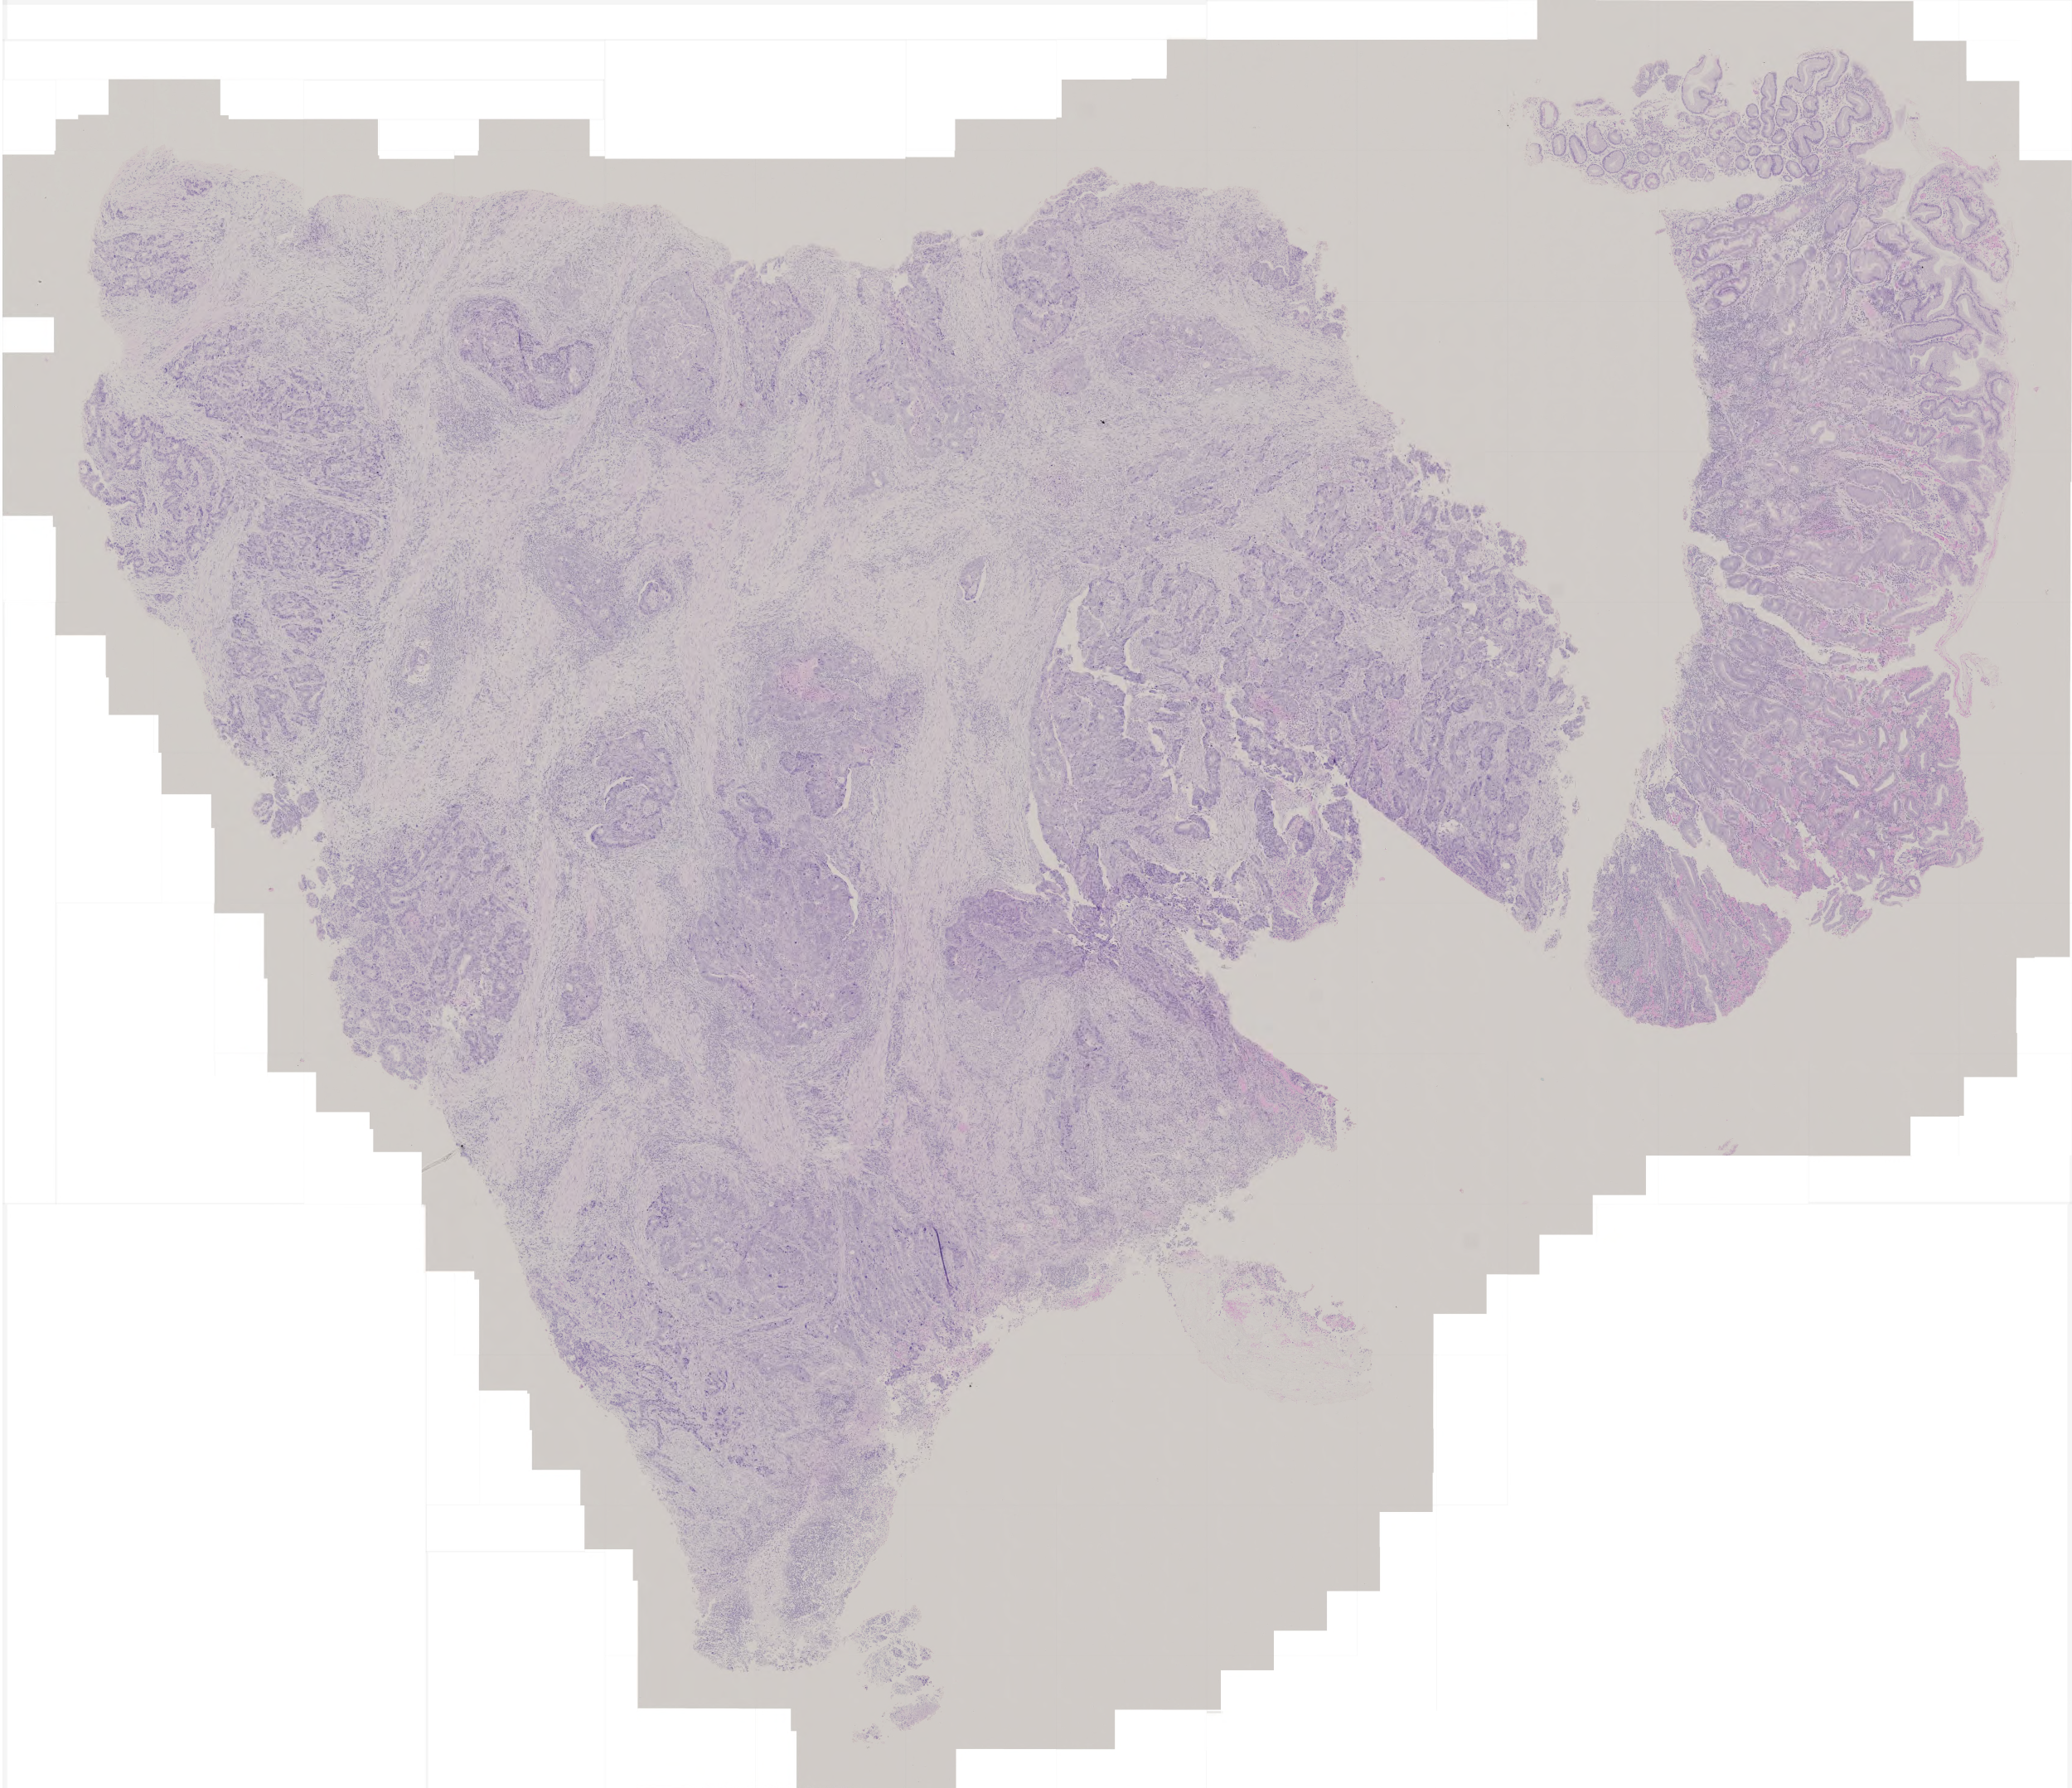
Whole-slide histology image, Hematoxylin and eosin (H&E) stained — shown as a low-resolution overview of the whole scanned area (about 5.0 x 4.3 mm), formalin-fixed paraffin-embedded (FFPE) diagnostic section, sample: primary tumour, stomach. Male, age 68 years at initial diagnosis. Histologic grade: G3 (poorly differentiated).
• AJCC pathologic stage: IIIA (5th edition)
• pathologic diagnosis: Adenocarcinoma, intestinal type (body of stomach)